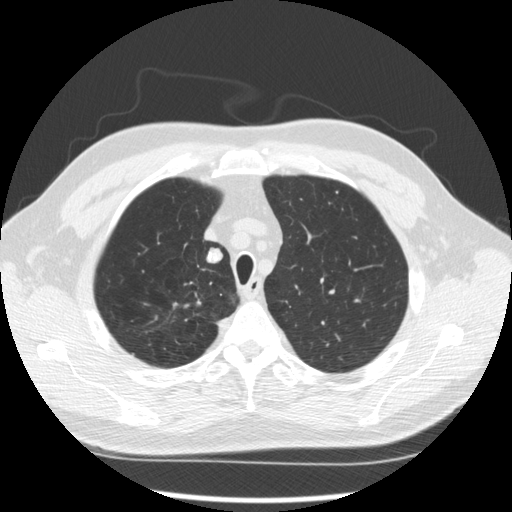
Axial slice from a low-dose chest CT screening exam; second annual screen; lung window (W 1500 / L -600 HU); standard (soft-tissue) reconstruction kernel (STANDARD); 512 × 512 image matrix, field of view 360 × 360 mm. Male, age 64 years at enrolment. Former smoker at enrolment.
Expert reader's lesion annotation, bounding box (x1, y1, x2, y2) in pixels: (191, 245, 226, 273). The screening reader recorded 3 non-calcified nodules or masses ≥4 mm on this exam (right upper lobe, right upper lobe, right upper lobe); which of them this box marks is not recorded. Official screen result: positive, other. Lung cancer was diagnosed 411 days after this screen (after the third annual screen): adenocarcinoma, NOS, right upper lobe, moderately differentiated (G2), stage IA (AJCC 6th edition), 14 mm at pathology.